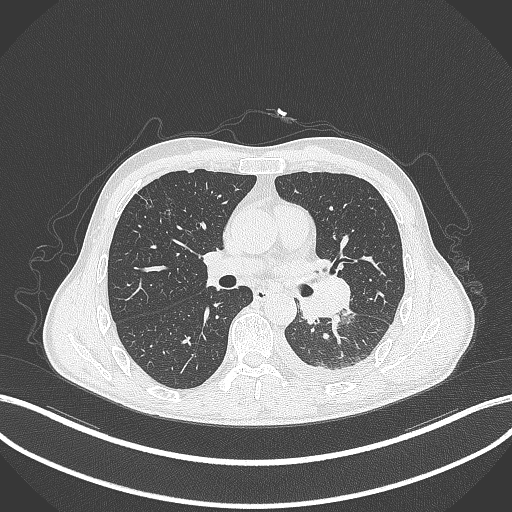
Chest CT, one axial slice; position 177 of 295 along the scan axis; reconstruction kernel B70f; lung window (W 1500 / L -600 HU); 1 mm slice thickness; 512 × 512 image matrix, field of view 400 × 400 mm. Patient: male, 47 years. From the clinical record (not read from this slice): clinical TNM (as recorded): T3 N1 M1c; histopathological grade: G3.
Annotated regions visible in this slice (rectangle marked by the reading radiologist):
- lung tumour (recorded histology: small cell carcinoma): bounding box [x1, y1, x2, y2] px = [293, 273, 354, 327]